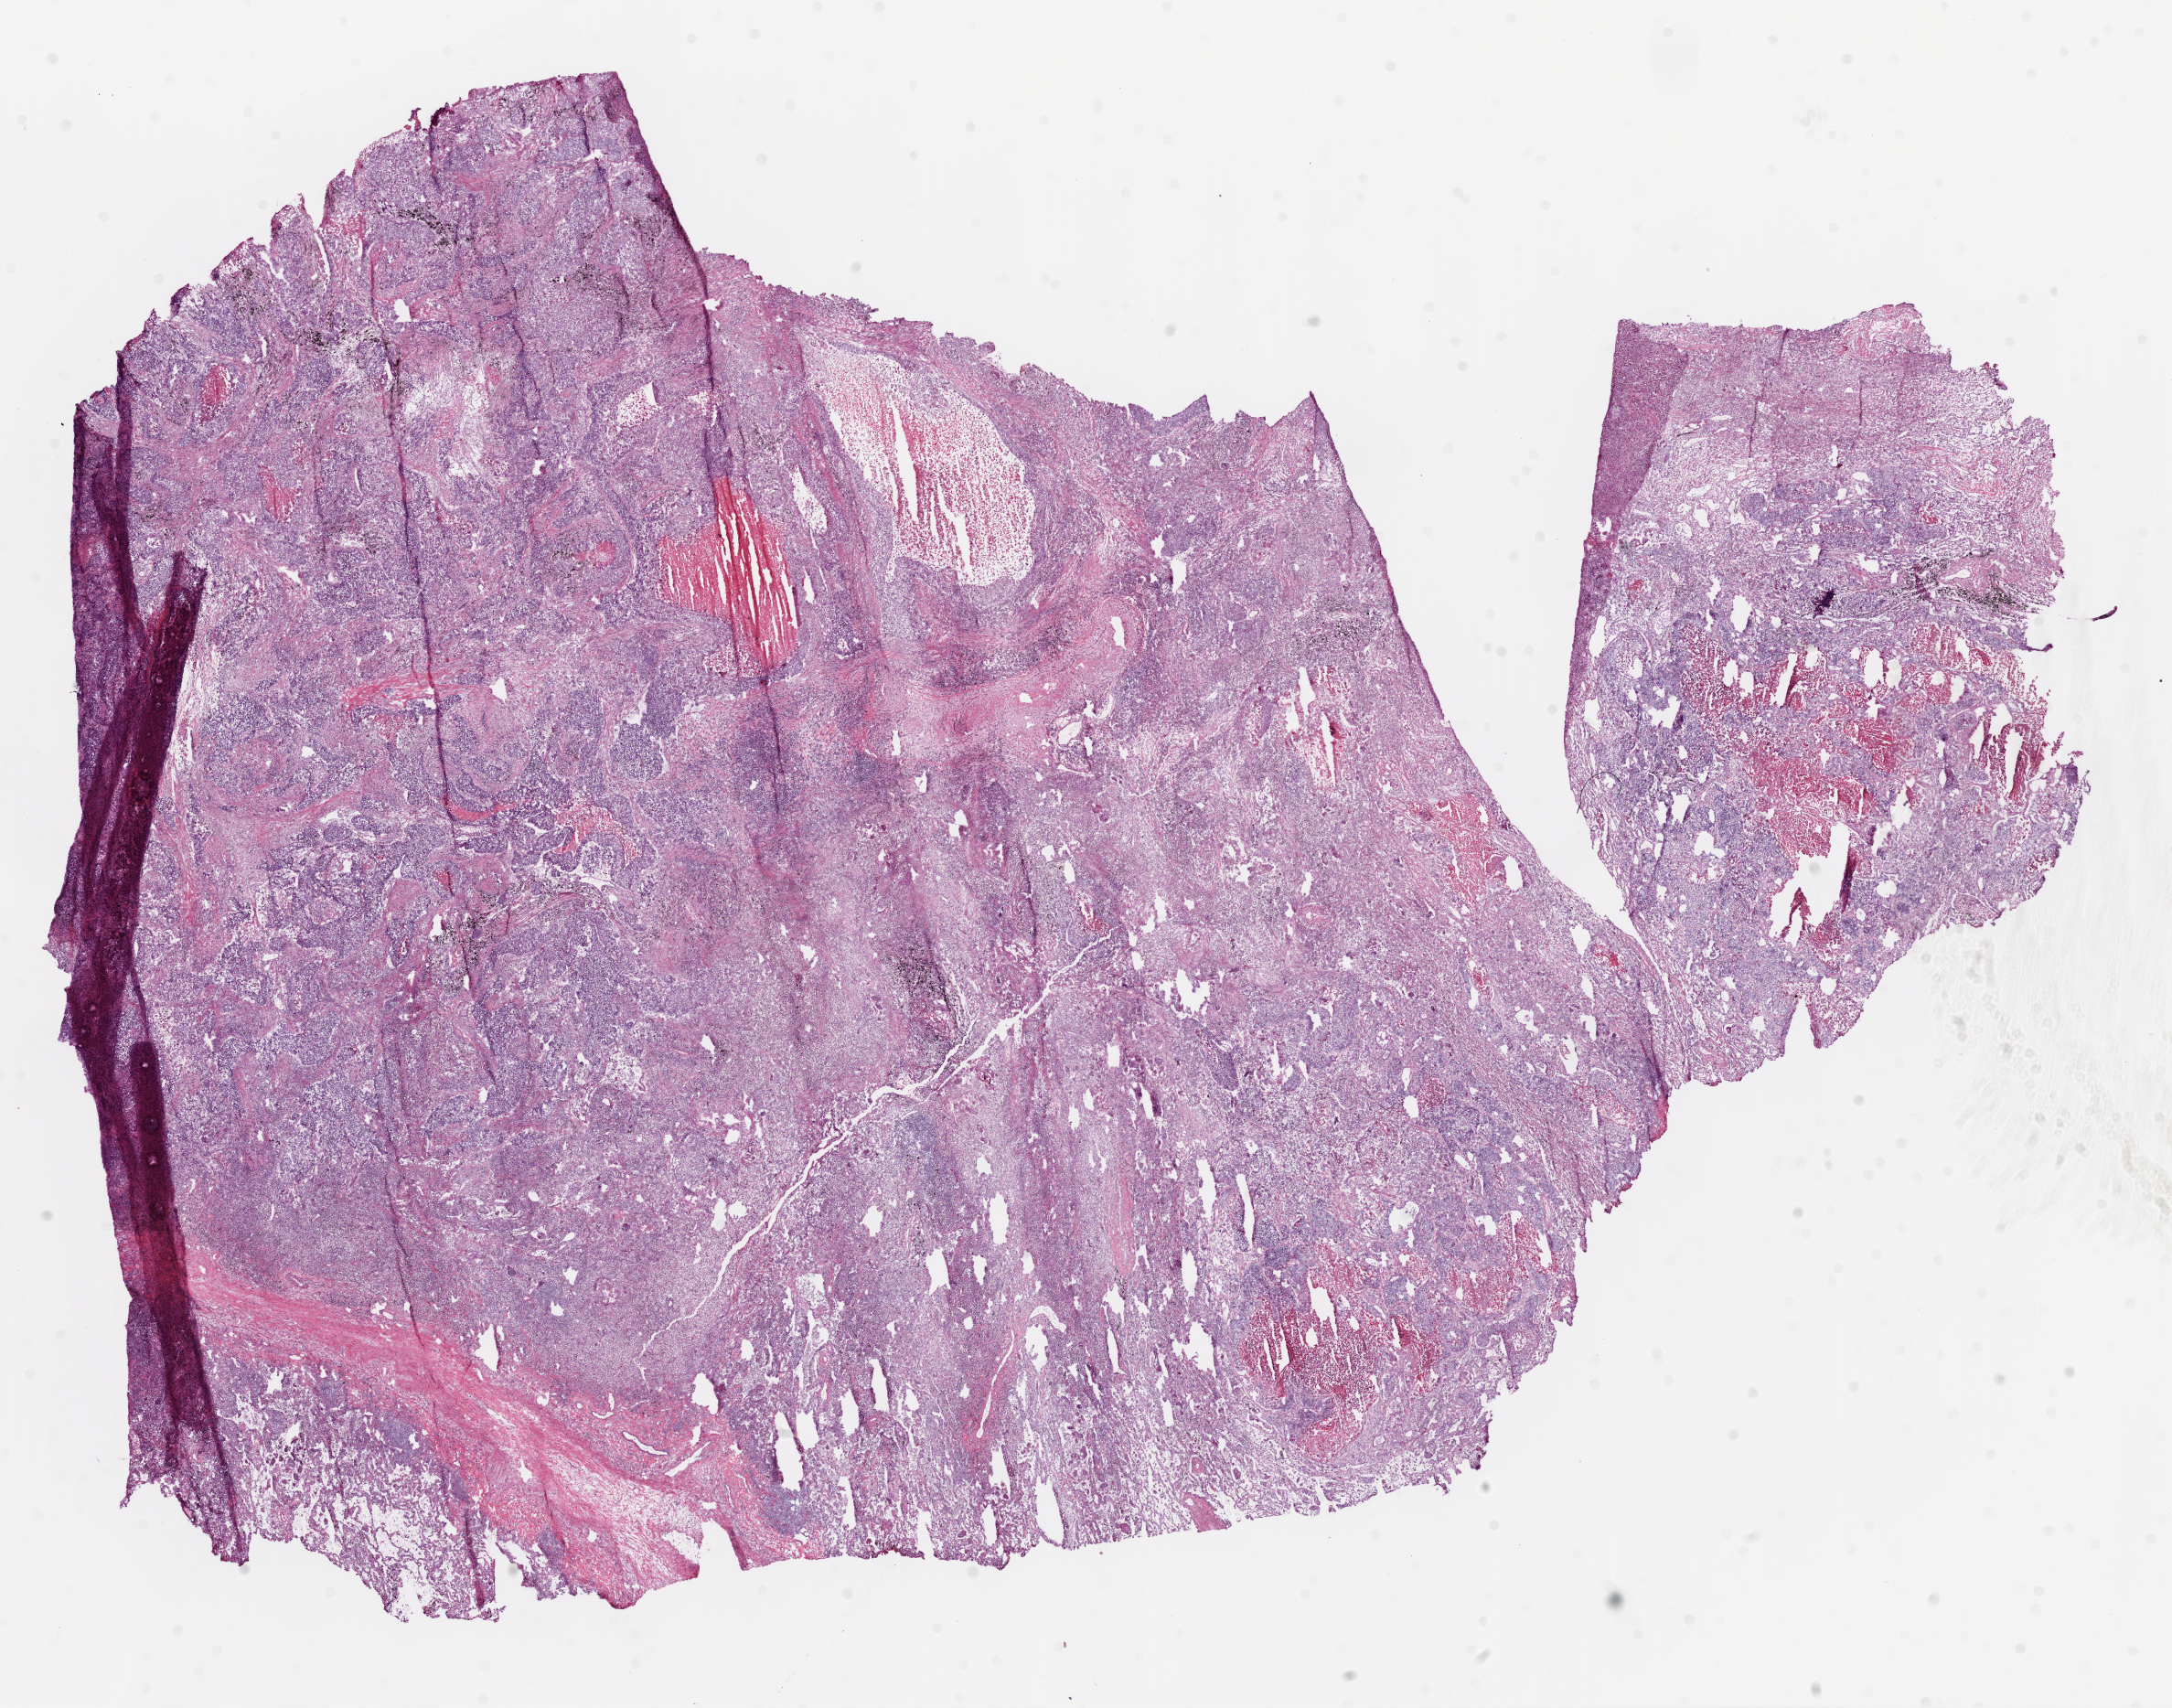
Hematoxylin and eosin (H&E) stained whole-slide image — shown as a low-resolution overview of the whole scanned area (about 19.1 x 15.0 mm); frozen section; primary tumour sample from the lung. Patient: male, age at initial diagnosis 69 years. Composition of this section per pathologist review: tumour cells 78%, tumour nuclei 60%, normal cells 0%, stromal cells 15%, necrosis 7%.
* pathologic diagnosis: Squamous cell carcinoma, NOS (upper lobe, lung)
* AJCC pathologic stage: IB (6th edition)